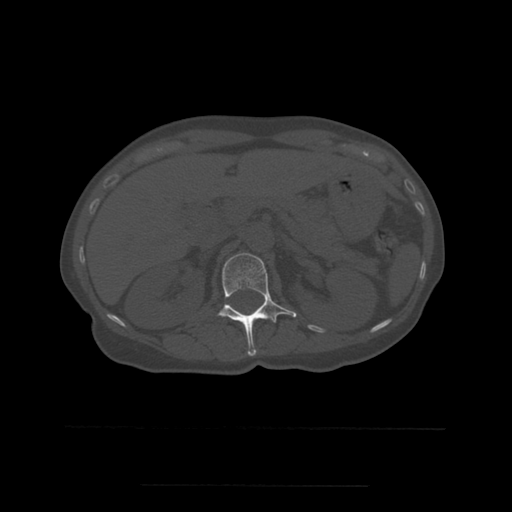
CT including the spine, one axial slice; position 236 of 544 along the scan axis; bone window (W 1800 / L 400 HU); 1.25 mm slice thickness; 512 × 512 image matrix, field of view 350 × 350 mm. Patient age 58 years. From the clinical record (not read from this slice): primary cancer: lung.
Outlined on this slice (semi-automatically segmented with operator editing):
- L1 vertebra: bounding box <217,253,297,356> (left, top, right, bottom; pixels)